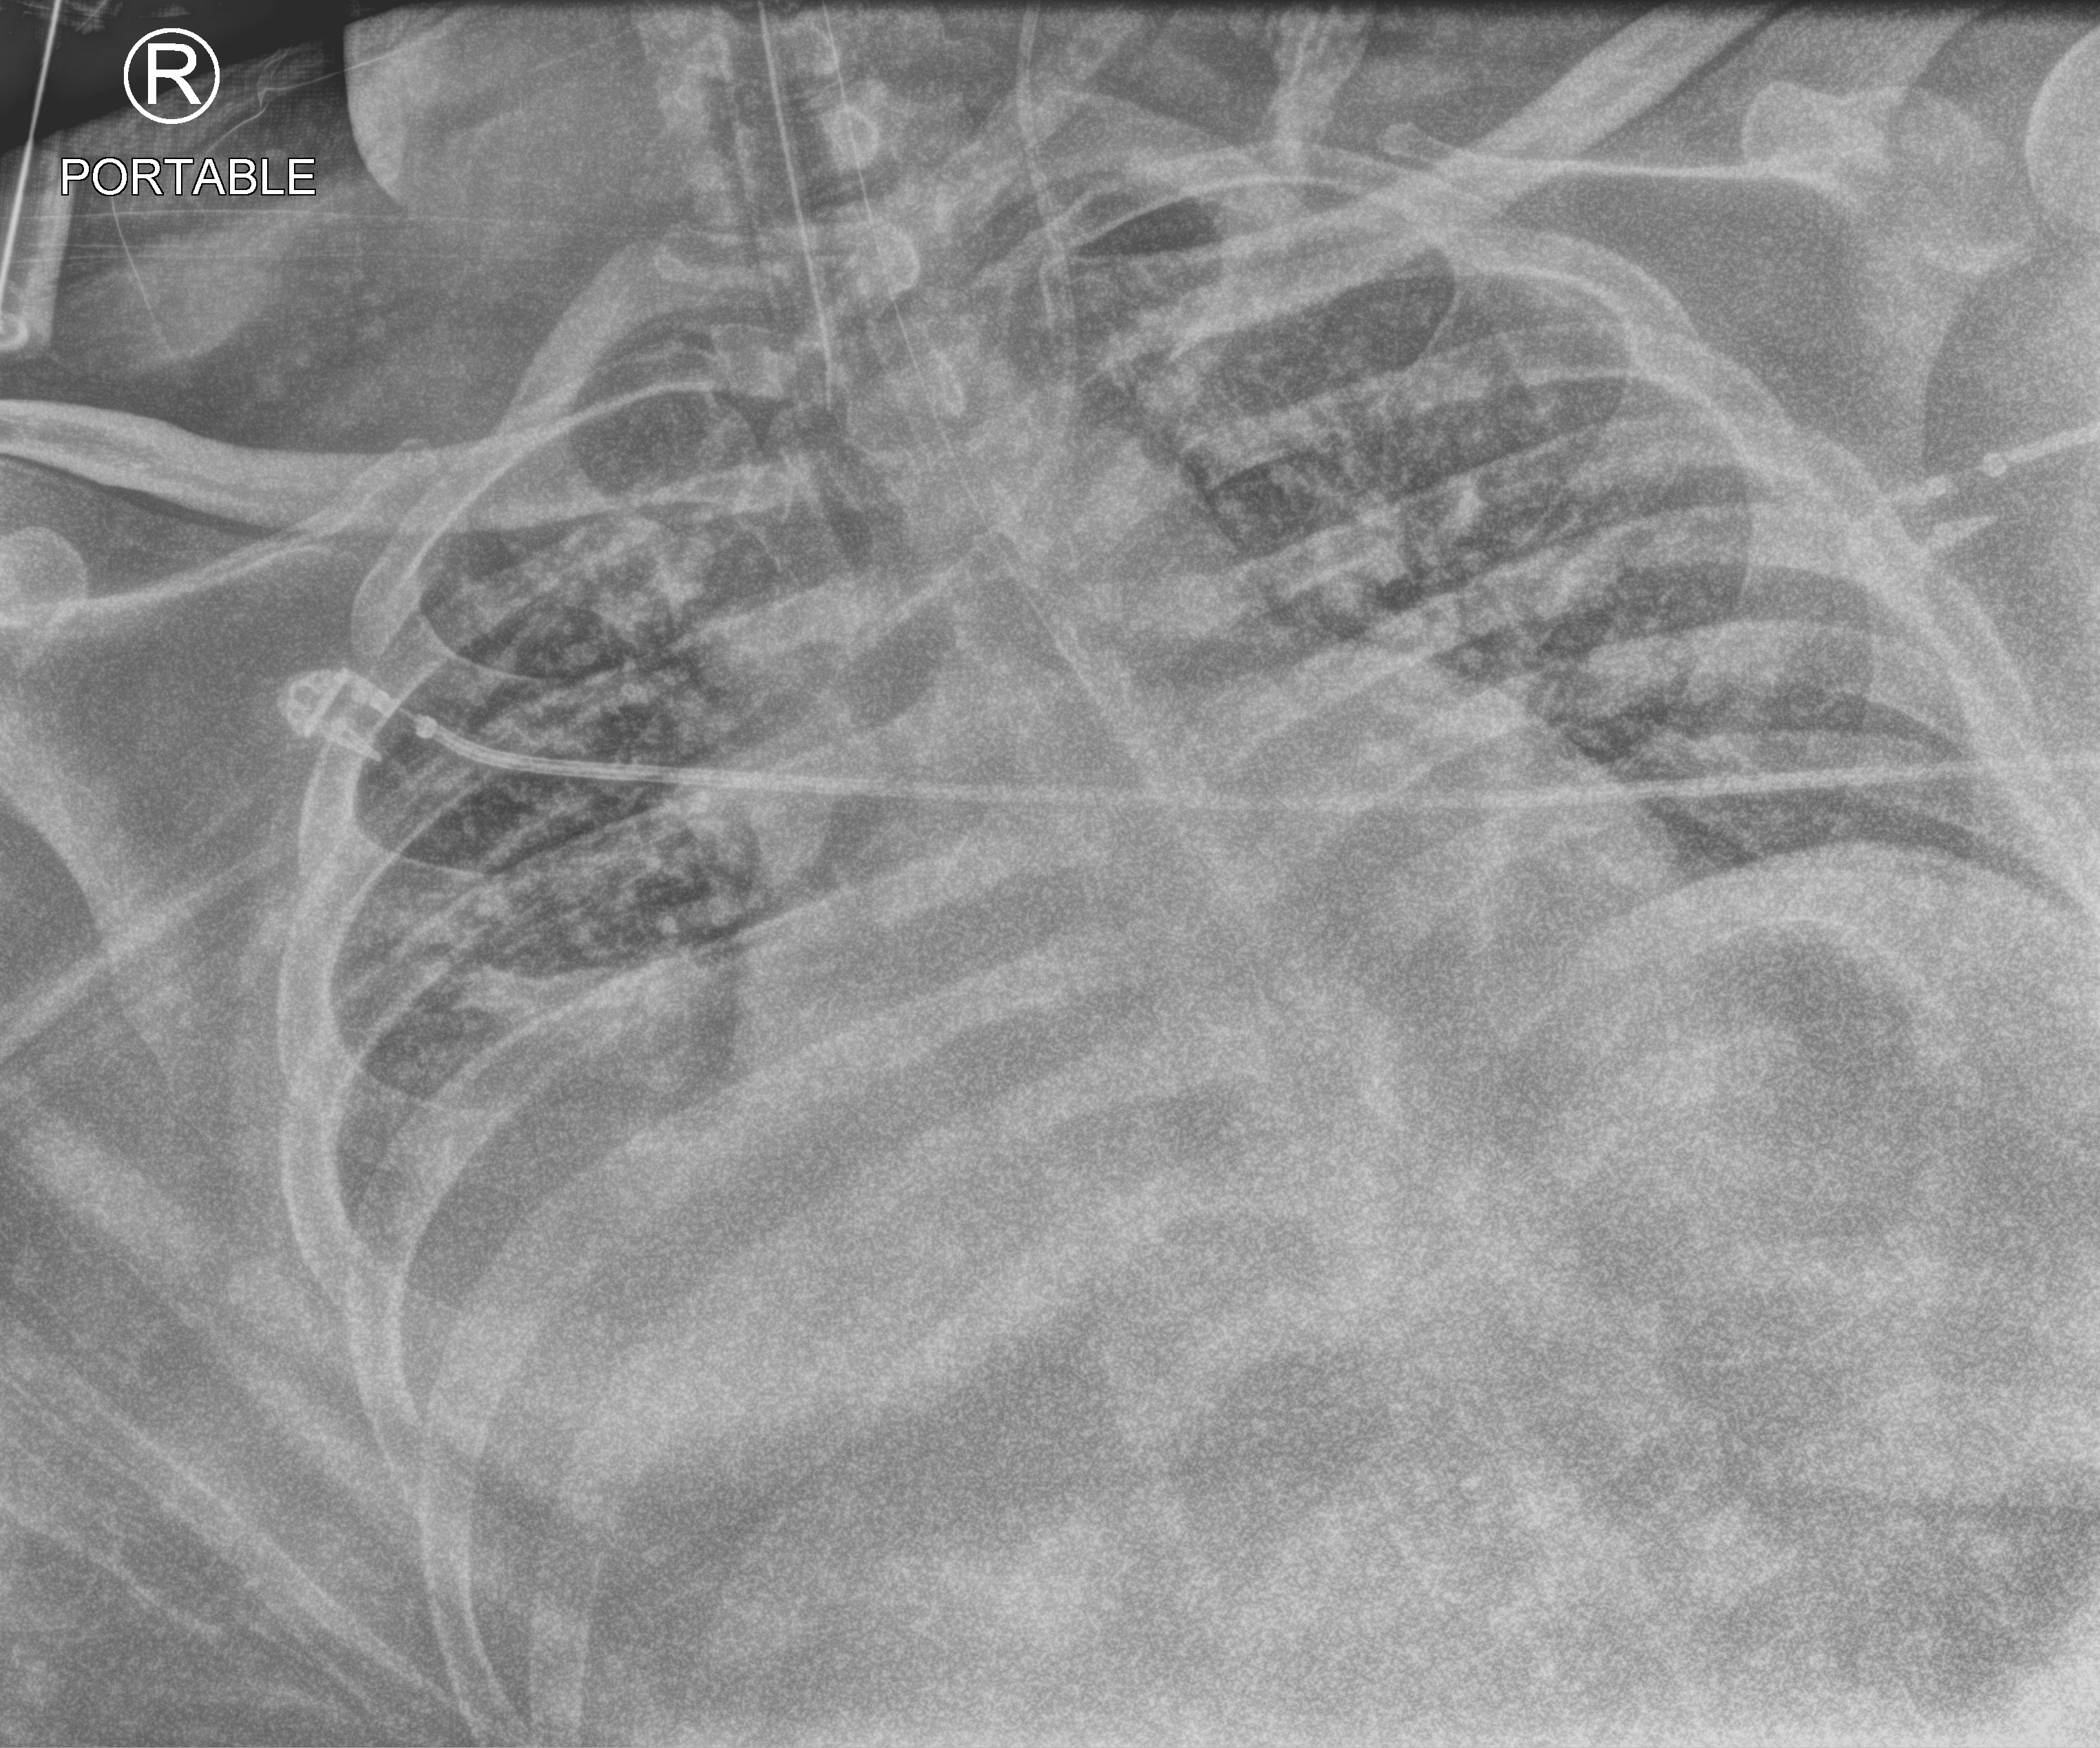
Chest X-ray (portable); anteroposterior (AP) projection. Male patient hospitalised with COVID-19, age 18–59 years.
From the hospital-stay record, not from the radiograph (when in the stay this image was taken is not recorded):
- mechanically ventilated during this hospital stay: yes
- hypertension (admission record): no